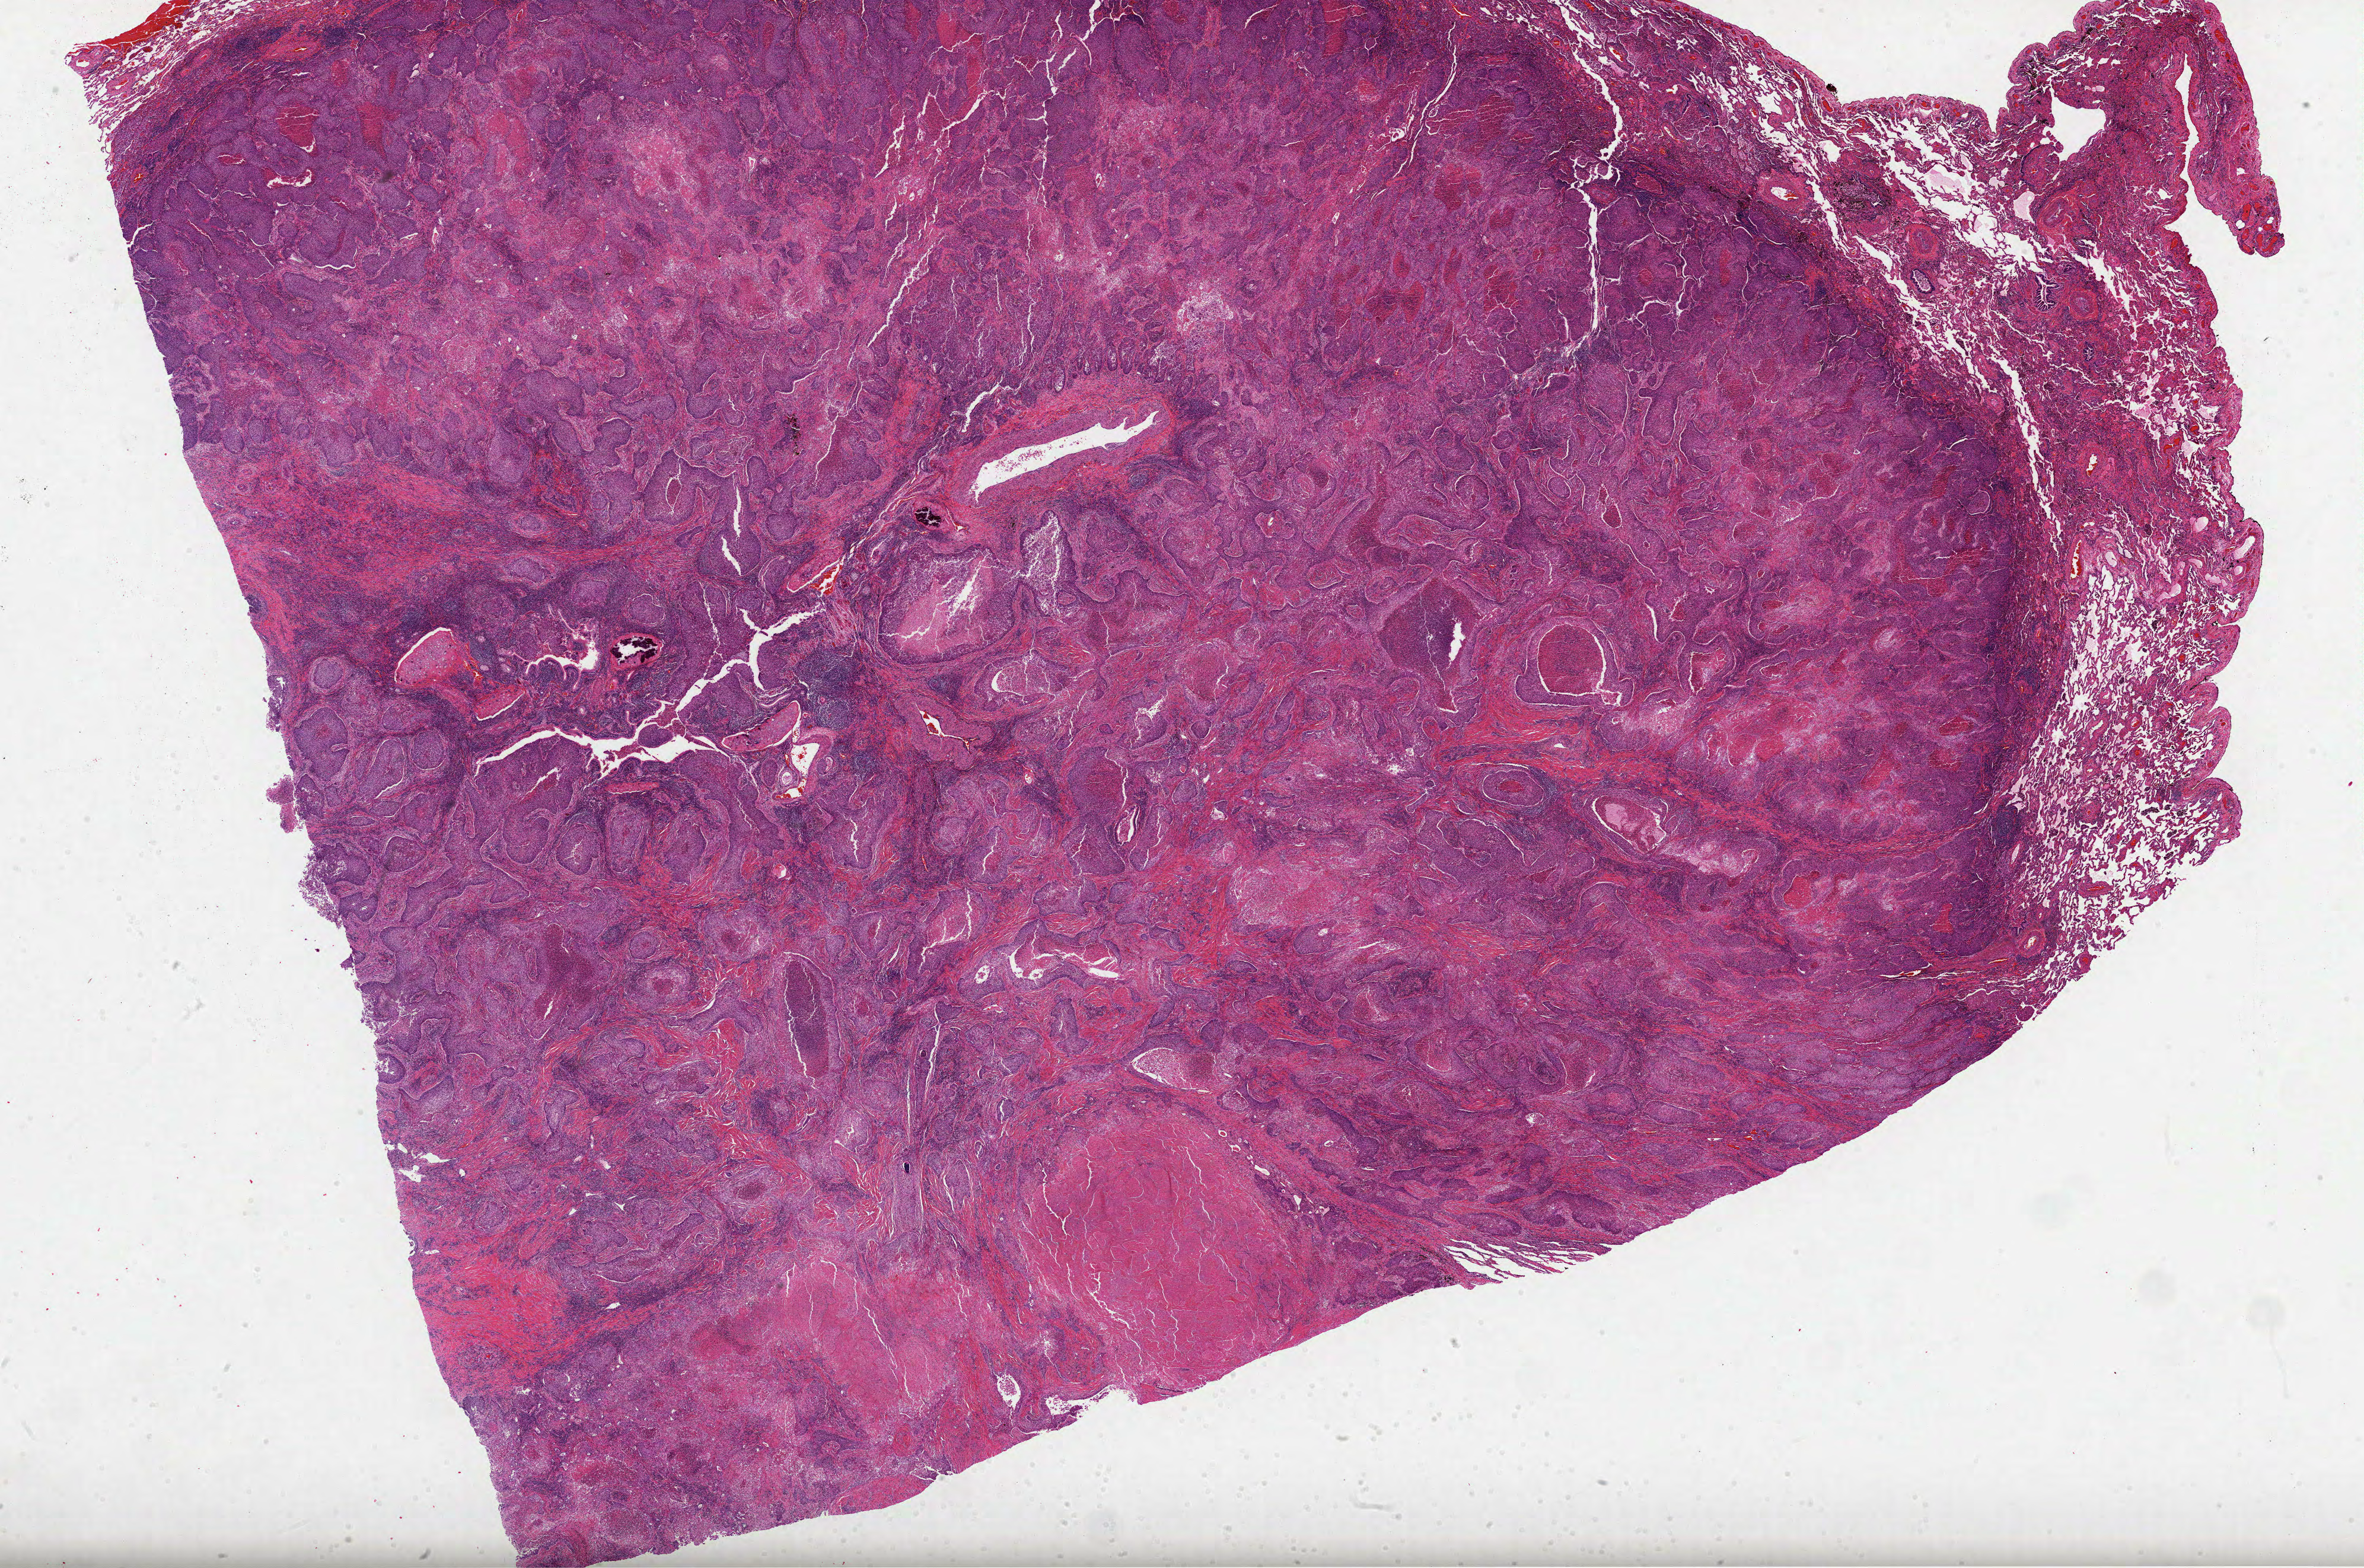
Digitized H&E tissue section (whole slide), whole scanned area (about 32.1 x 21.3 mm, slide scanned at 40x) shown as a low-resolution overview. Formalin-fixed paraffin-embedded (FFPE) diagnostic section. Lung, primary tumour sample. Male patient; age at initial diagnosis 68 years.
AJCC pathologic stage: IB (6th edition). Pathologic diagnosis: Squamous cell carcinoma, NOS (upper lobe, lung).